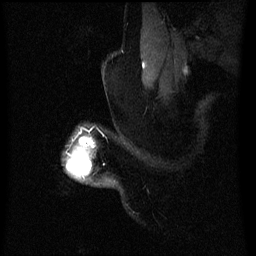
Breast MRI (dynamic contrast-enhanced), one sagittal slice. Dynamic contrast-enhanced series, image 2 of 3 at this slice position (ordered by acquisition). 1.5 T. TE 4.2 ms, TR 8 ms. 256 × 256 image matrix, field of view 200 × 200 mm. Patient: female, 50 years.
Structures marked on this image (semi-automatic segmentation, software-assisted and operator-edited):
- analysis volume of interest (the breast-tissue region the enhancement analysis was run in; not a lesion): bounding box <67,138,95,179> (left, top, right, bottom; pixels)
- tumour enhancement mask (voxels above the 70 % enhancement threshold inside the analysis volume of interest): <79,138,93,145>